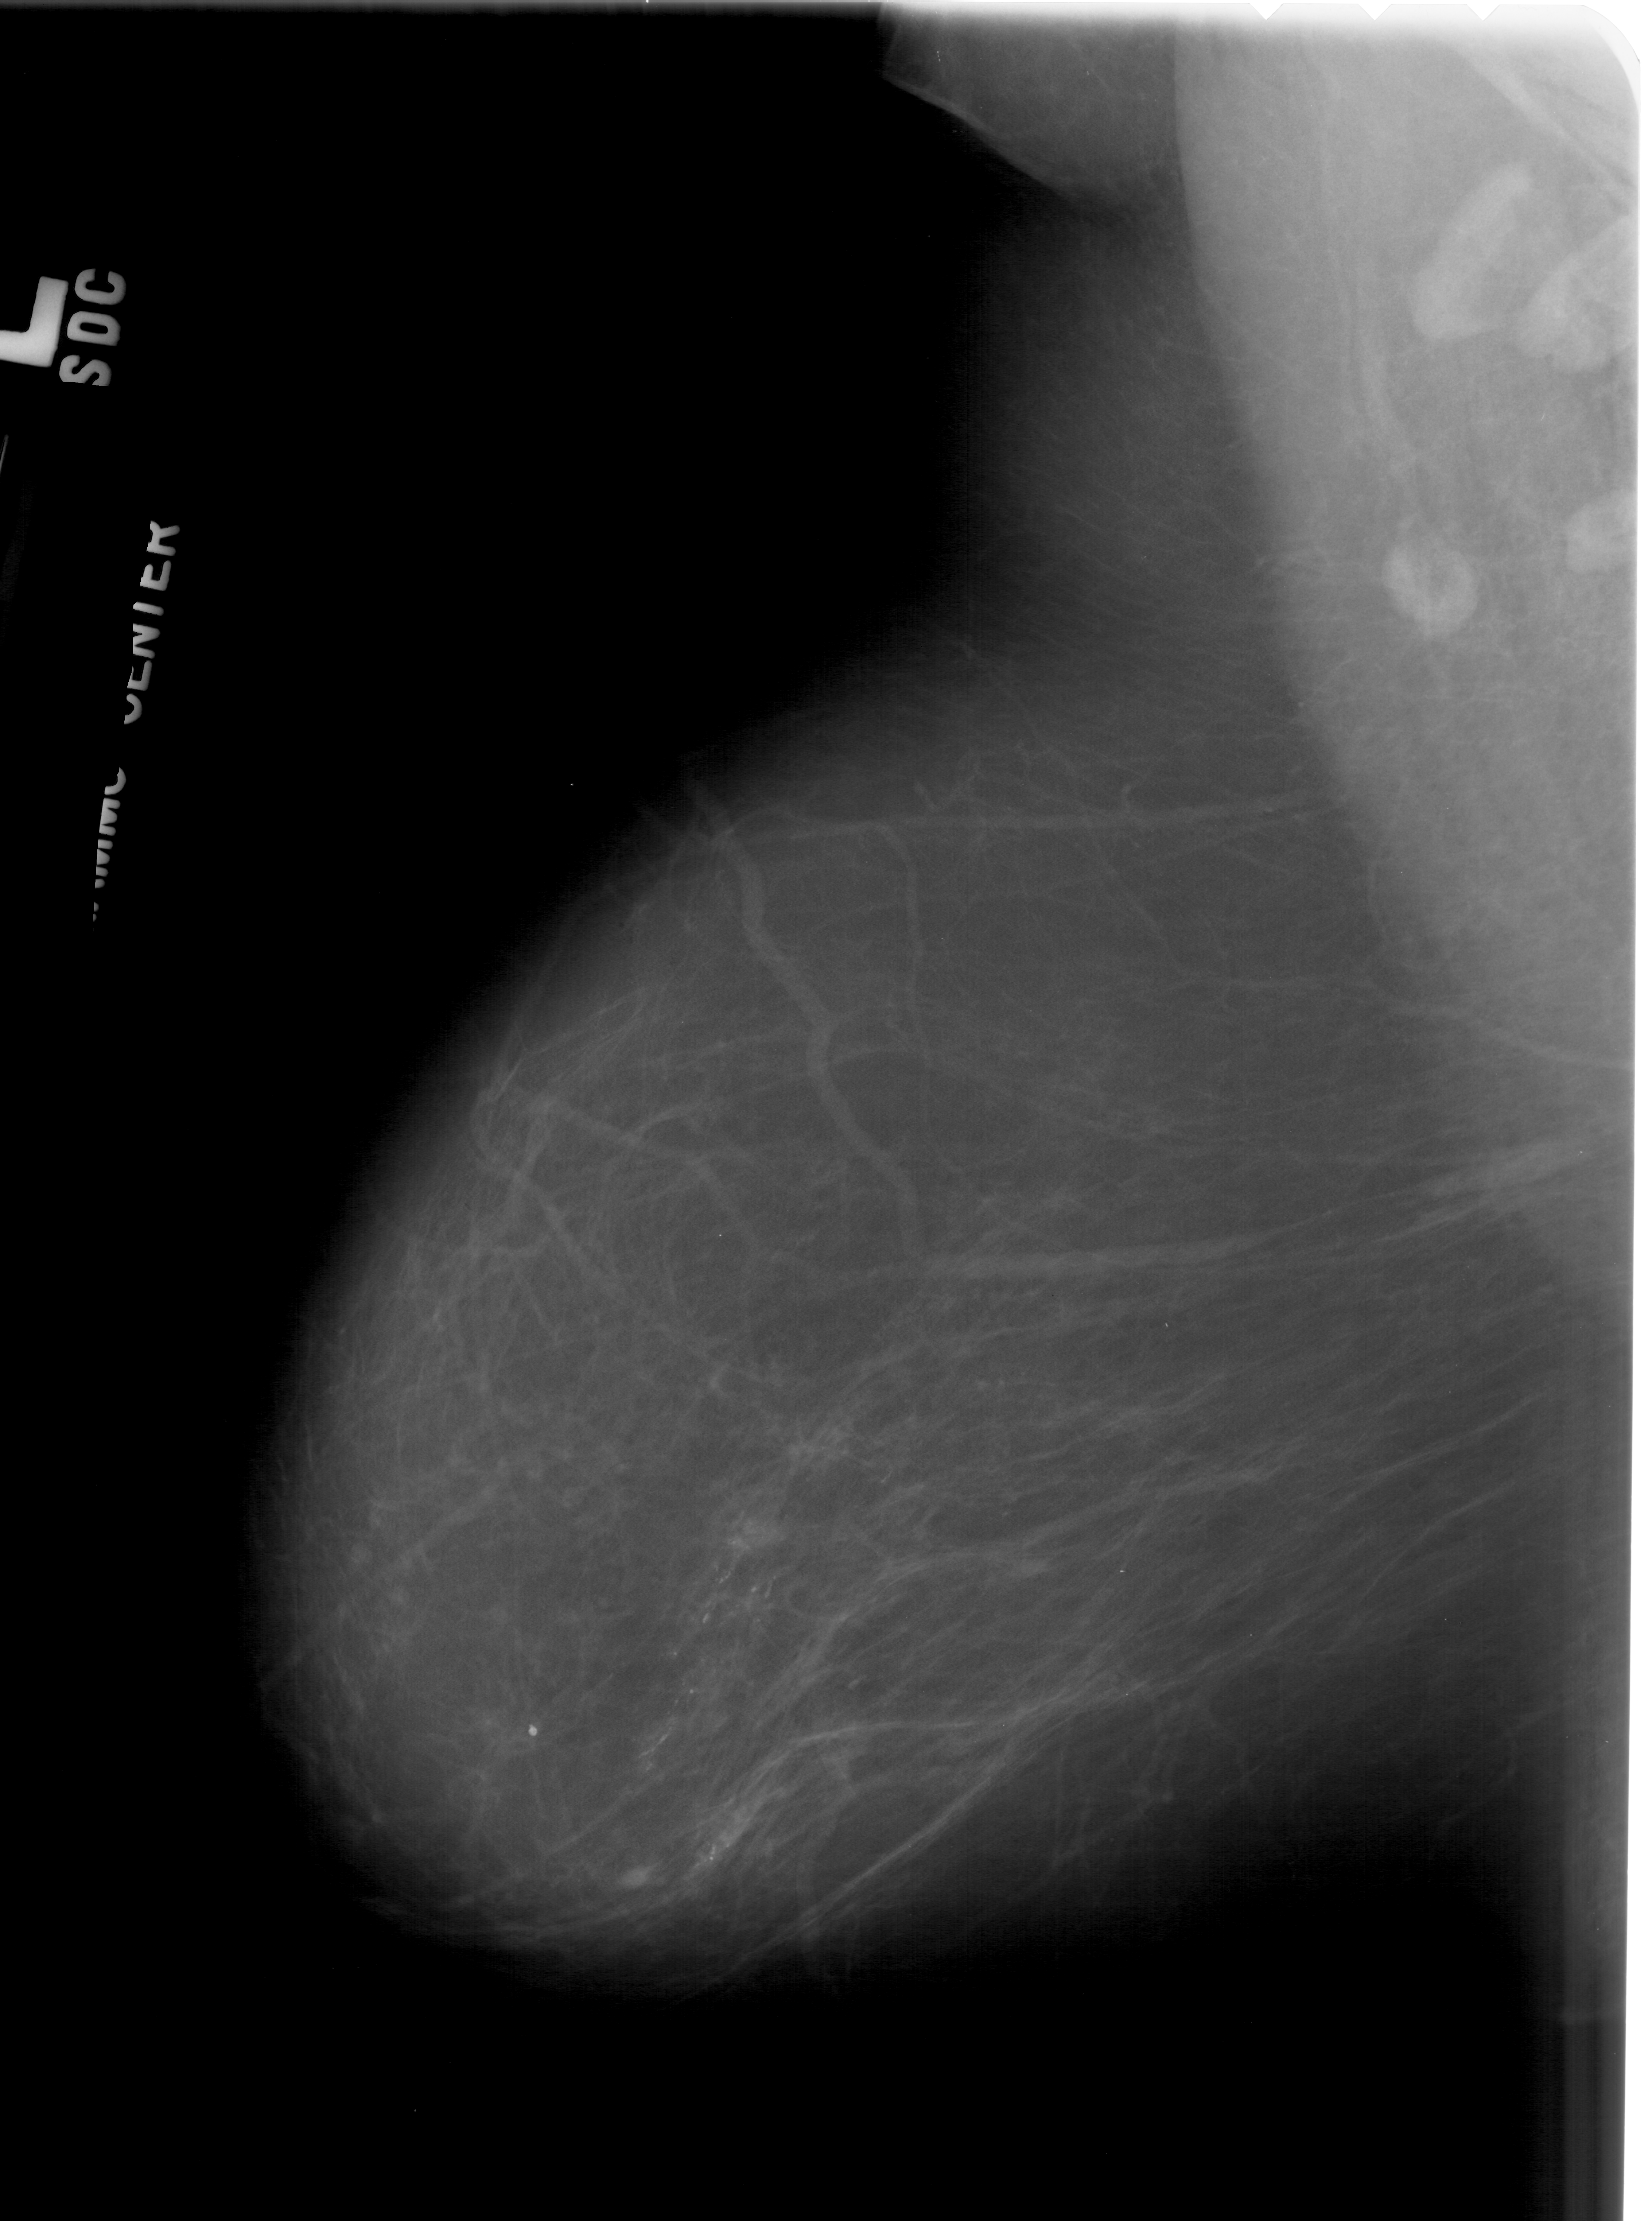
Scanned film-screen mammogram; left breast; mediolateral oblique (MLO) view; breast composition: scattered fibroglandular densities (BI-RADS density category 2 of 4).
Radiologist-marked abnormalities on this image: calcifications, morphology fine linear branching, distribution segmental; BI-RADS assessment category 5; subtlety rating 5 on a 1 (subtle) to 5 (obvious) scale; pathology (as recorded): malignant.